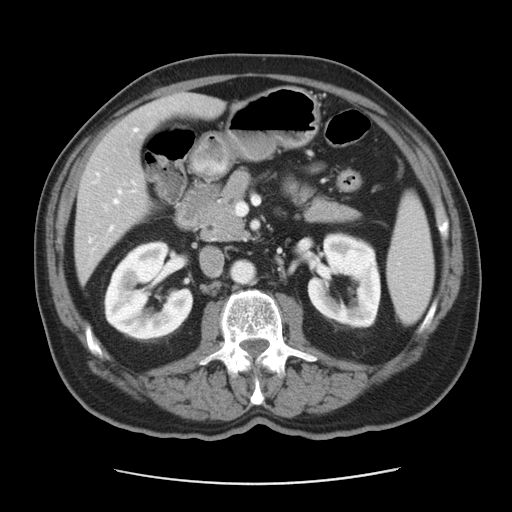
Contrast-enhanced abdominal CT, one axial slice. Slice 19 of 42 in the series (ordered by position). Reconstruction kernel STANDARD. 120 kVp. Soft-tissue window (W 400 / L 40 HU). 5 mm slice thickness. 512 × 512 image matrix, field of view 370 × 370 mm. Male patient, age 73 years. From the clinical record (not read from this slice): diagnosis: colorectal cancer liver metastases, imaged before liver resection; multiple liver metastases: yes; largest metastasis: 0.5 cm.
Annotated regions visible in this slice (expert manual segmentation):
- hepatic veins: bounding box [x1, y1, x2, y2] px = [88, 129, 137, 243]
- liver: [76, 95, 221, 277]
- planned liver remnant (the part of the liver to remain after resection): [110, 95, 222, 159]
- portal vein (with intrahepatic branches): [110, 226, 113, 230]